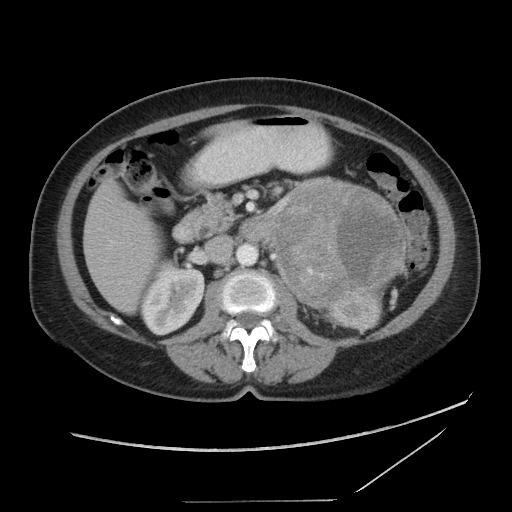
Contrast-enhanced abdominal CT, one axial slice. Reconstruction kernel STANDARD. Intravenous contrast given. Soft-tissue window (W 400 / L 40 HU). 5 mm slice thickness. 512 × 512 image matrix. Female patient, age 77 years. Case-level facts recorded for this patient, not image findings: diagnosis: adrenocortical carcinoma; tumour side: left adrenal; tumour size at pathology: 13.1 cm; Ki-67 index: 10 %; stage (as recorded): 3.
Annotated regions visible in this slice (semi-automatic segmentation, software-assisted and operator-edited):
- mass: box from (x=274, y=181) to (x=403, y=306) px